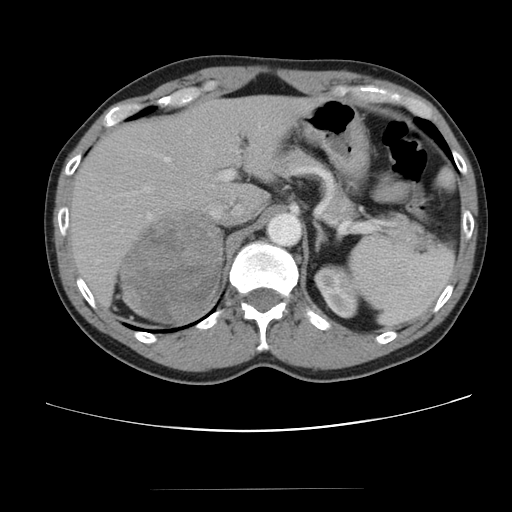
Contrast-enhanced abdominal CT, one axial slice; intravenous contrast given; soft-tissue window (W 400 / L 40 HU); 5 mm slice thickness; 512 × 512 image matrix, field of view 360 × 360 mm. Patient: male, 61 years. From the clinical record (not read from this slice): diagnosis: adrenocortical carcinoma; tumour side: right adrenal; tumour size at pathology: 11.1 cm; Ki-67 index: 32 %; stage (as recorded): 2.
Structures marked on this image (semi-automatic segmentation, software-assisted and operator-edited):
- mass: bounding box <121,211,221,321> (left, top, right, bottom; pixels)